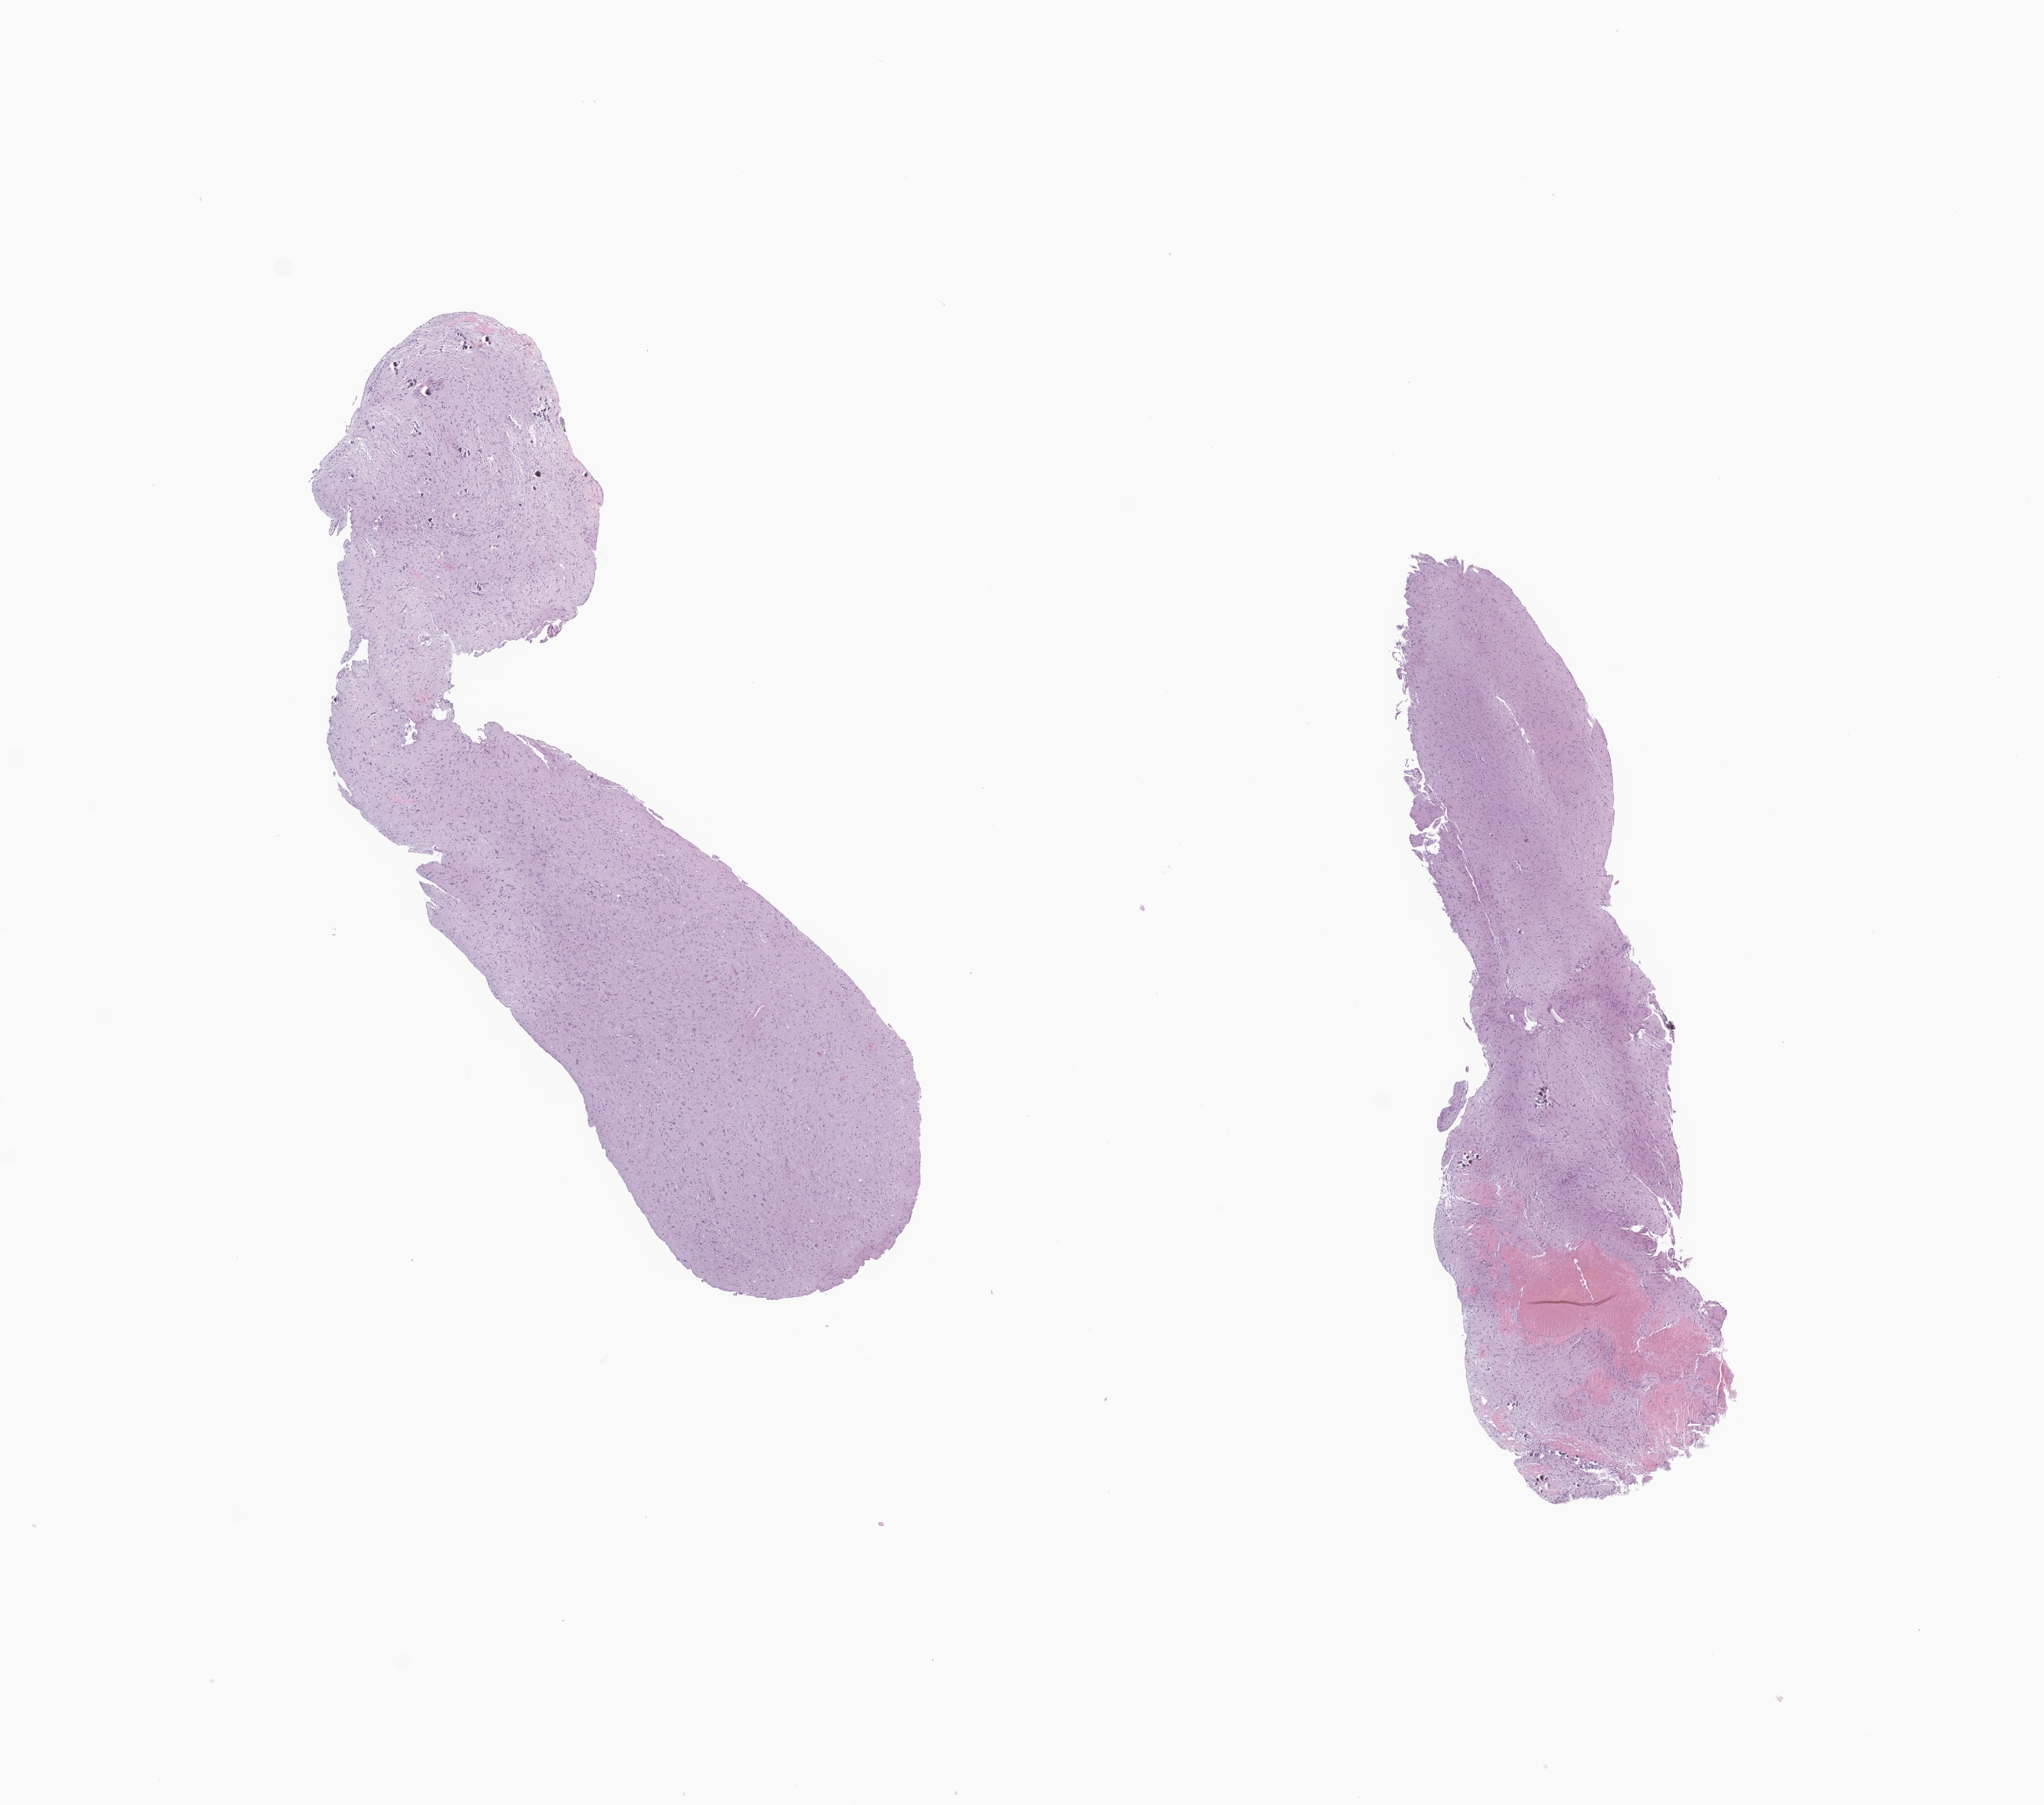
H&E whole-slide image of tumor tissue from the brain, low-resolution overview of the scanned area, about 12.2 x 10.8 mm; formalin-fixed paraffin-embedded section. Female patient, age 267 months.
Diagnosis (ICD-O-3 morphology term): Neoplasm, malignant.